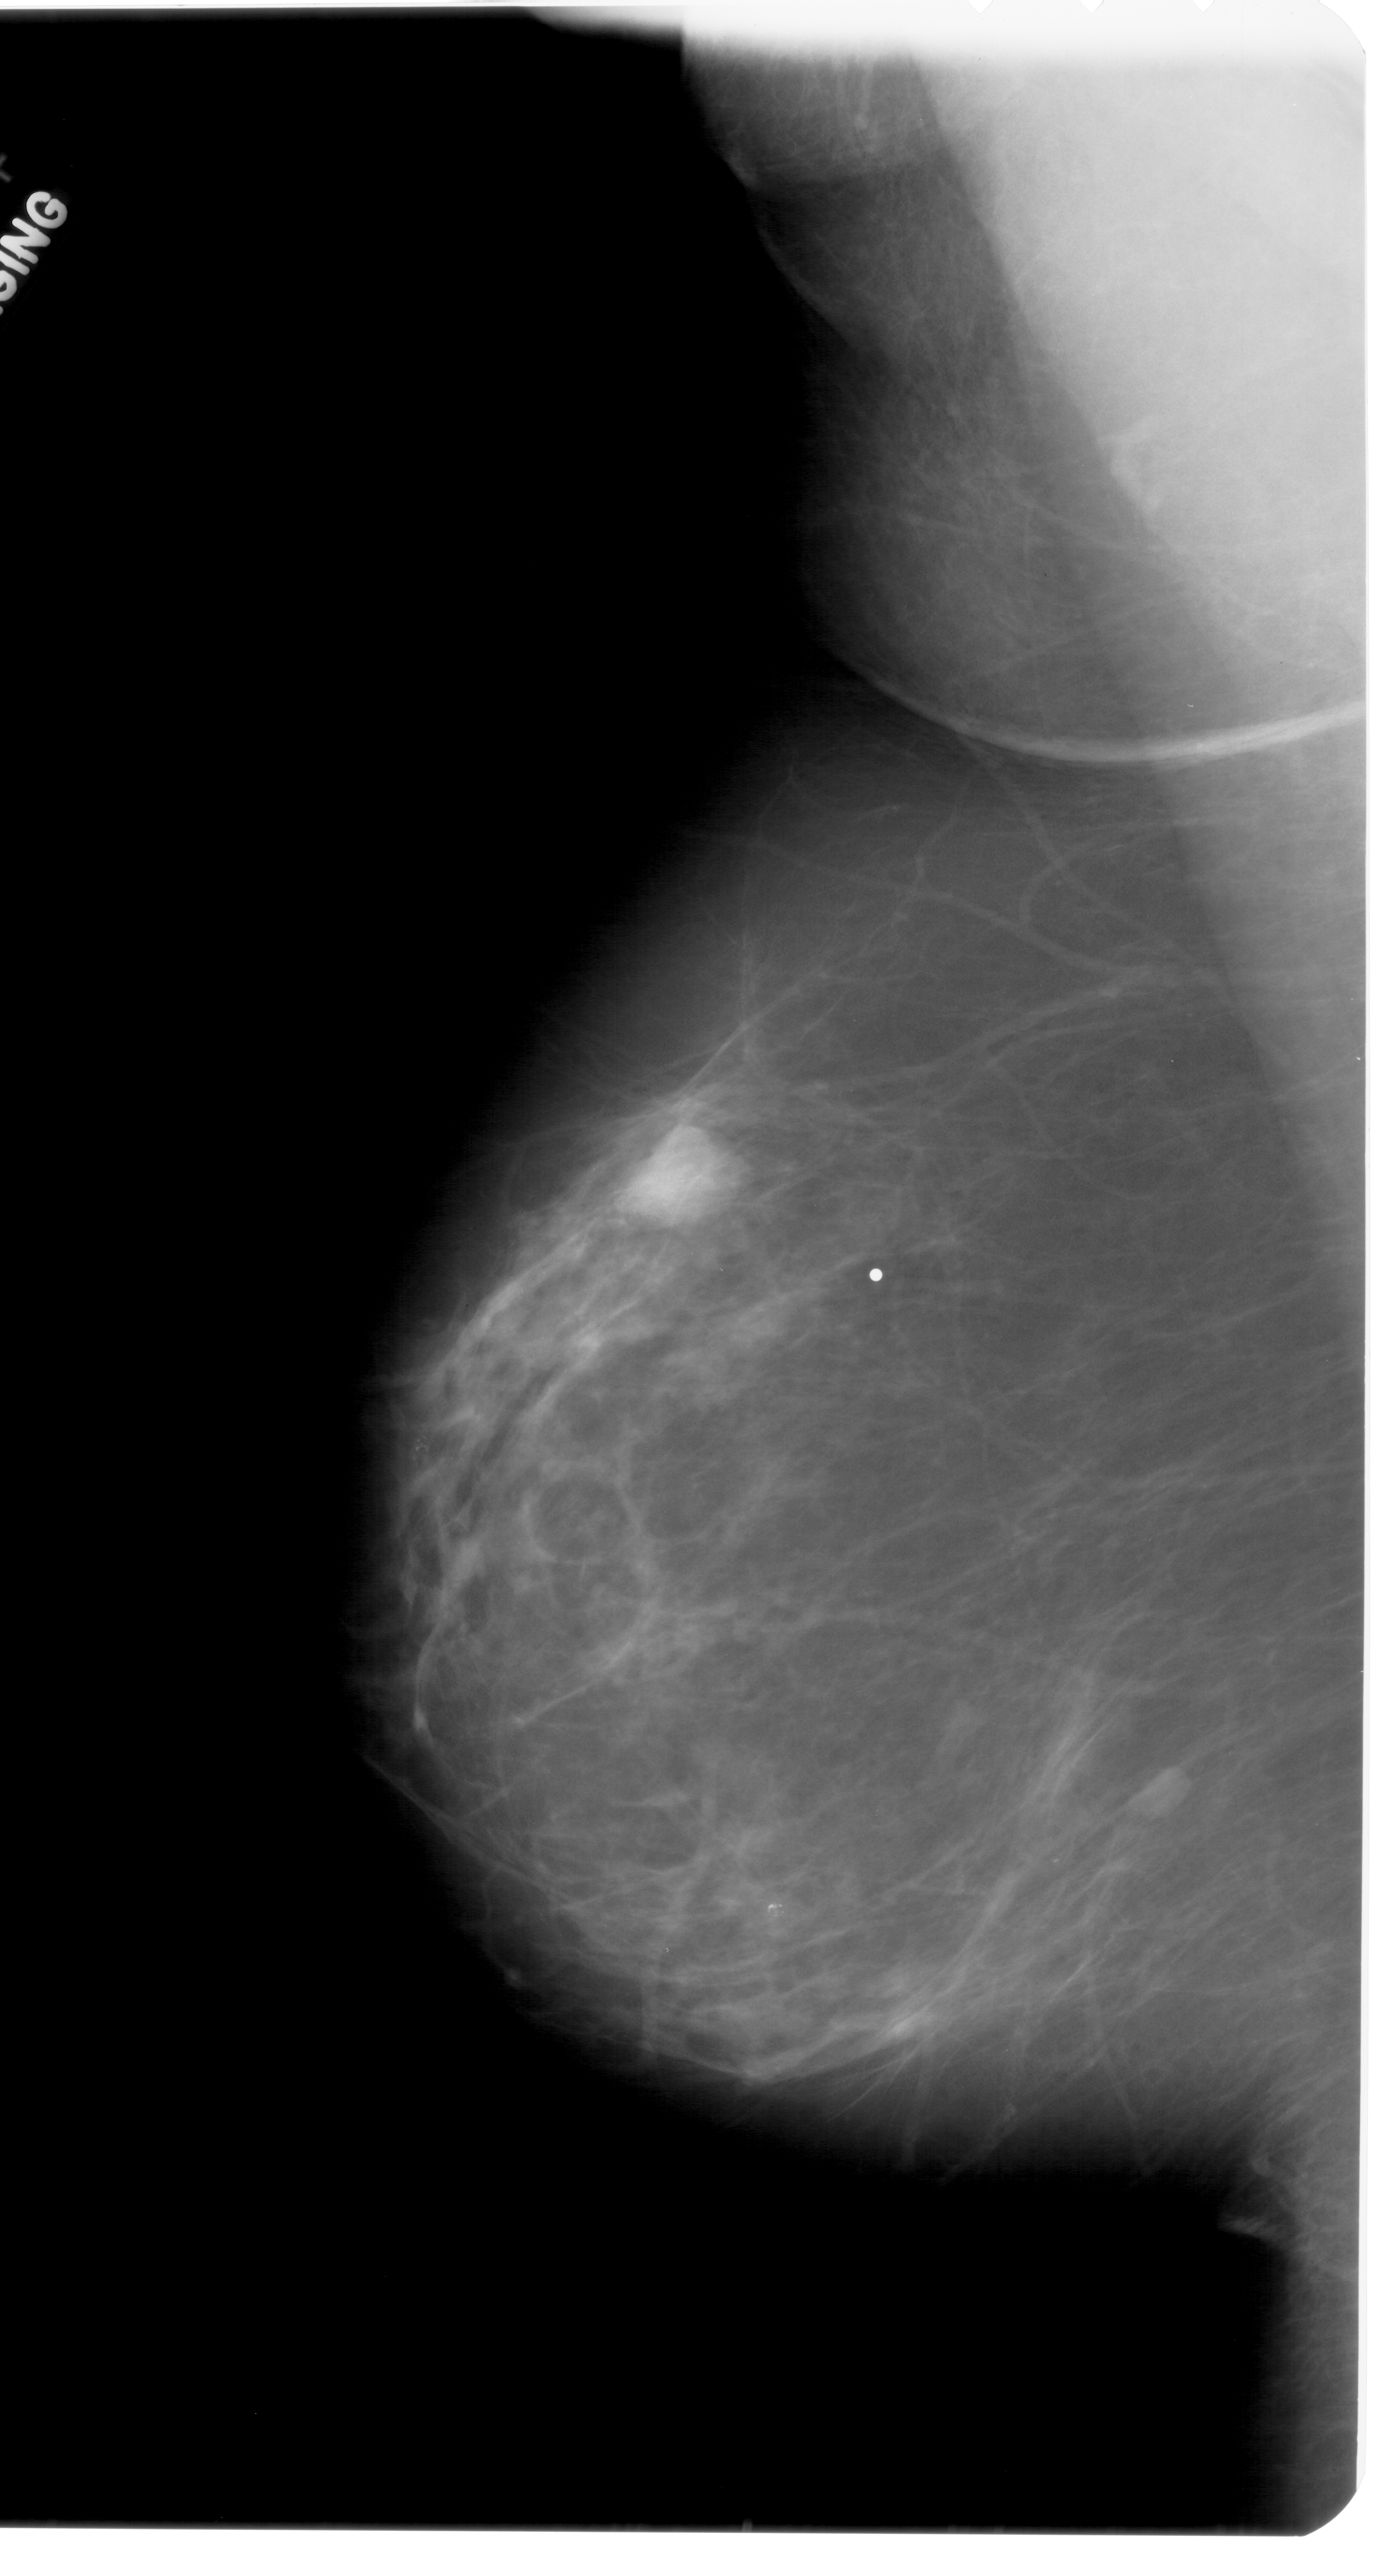
Digitized screen-film mammogram; left breast; mediolateral oblique (MLO) view; breast composition: scattered fibroglandular densities (BI-RADS density category 2 of 4).
Marked abnormality: mass, shape lobulated, margins circumscribed; BI-RADS assessment category 4; subtlety rating 5 on a 1 (subtle) to 5 (obvious) scale; pathology result (as recorded, not read from the image): benign.